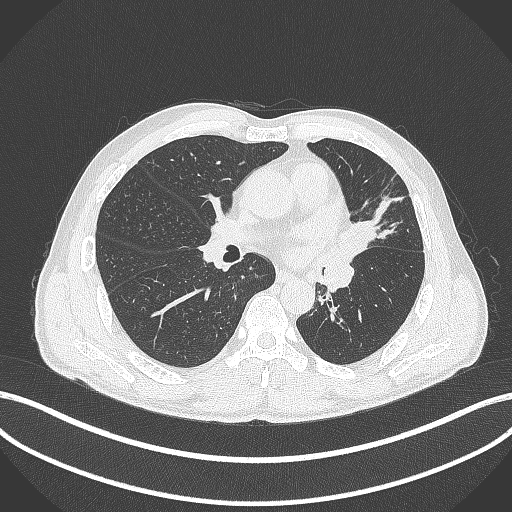
Chest CT, one axial slice; slice 225 of 429 in the series (ordered by position); 120 kVp; lung window (W 1500 / L -600 HU); 512 × 512 image matrix, field of view 400 × 400 mm. Male patient, age 57 years. Case-level facts recorded for this patient, not image findings: clinical TNM (as recorded): T2b N0 M0.
Outlined on this slice (bounding box drawn by a radiologist):
- lung tumour (recorded histology: squamous cell carcinoma): box from (x=333, y=210) to (x=377, y=262) px